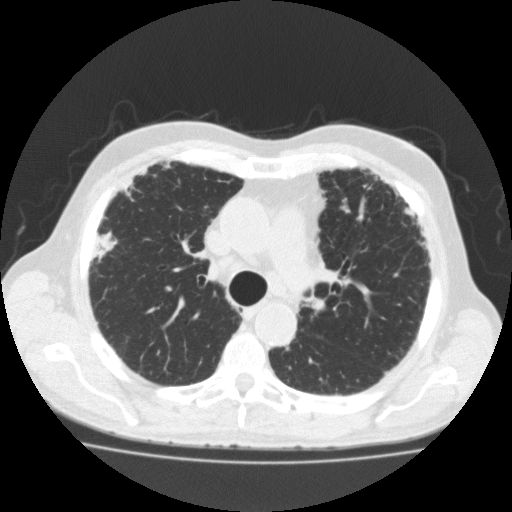
Low-dose screening chest CT, one axial slice; position 129 of 188 along the scan axis; lung window (W 1500 / L -600 HU); 2 mm slice thickness; 512 × 512 image matrix.
Annotated regions visible in this slice (expert manual segmentation):
- lesion 1 (tumor, upper lobe of right lung): box from (x=100, y=234) to (x=117, y=249) px